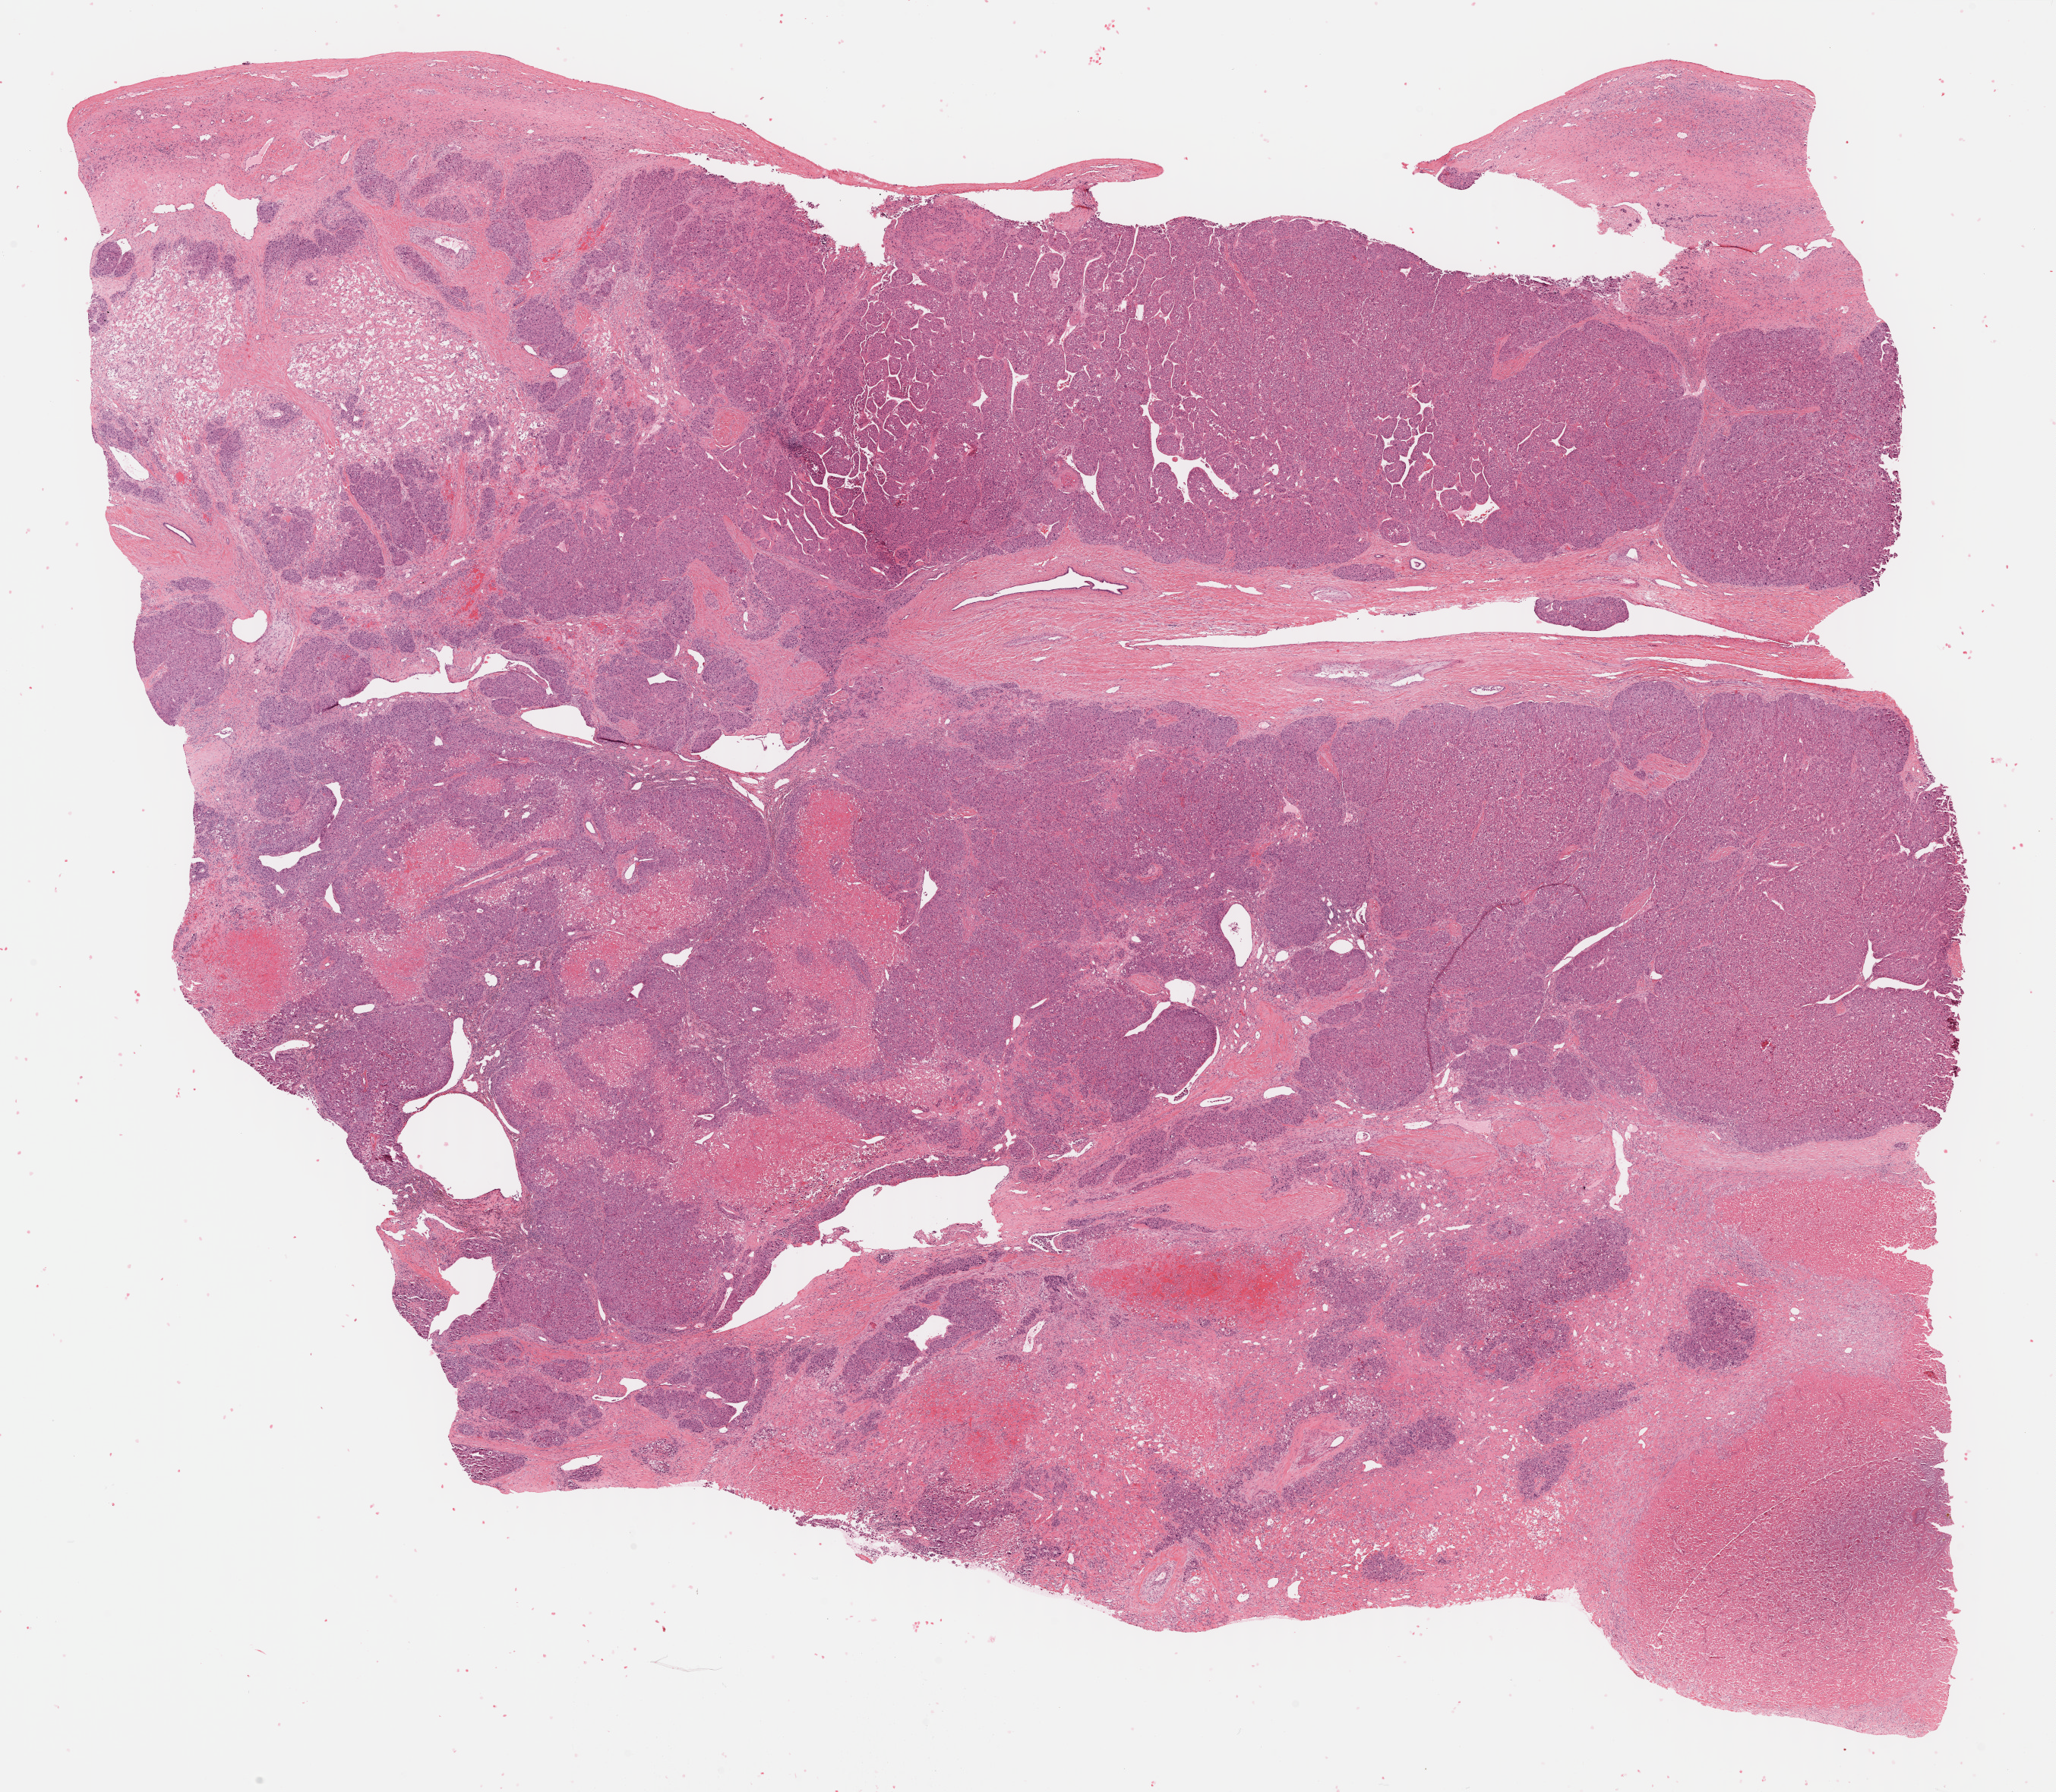
H&E whole-slide image, shown as a low-resolution overview of the whole scanned area (about 21.9 x 19.1 mm, from a 40x scan), formalin-fixed paraffin-embedded (FFPE) diagnostic section, primary tumour sample from the liver. Patient: male, age at initial diagnosis 67 years. Histologic grade: G3 (poorly differentiated).
Histologic diagnosis: Hepatocellular carcinoma, NOS. AJCC pathologic stage: IIIB (7th edition).